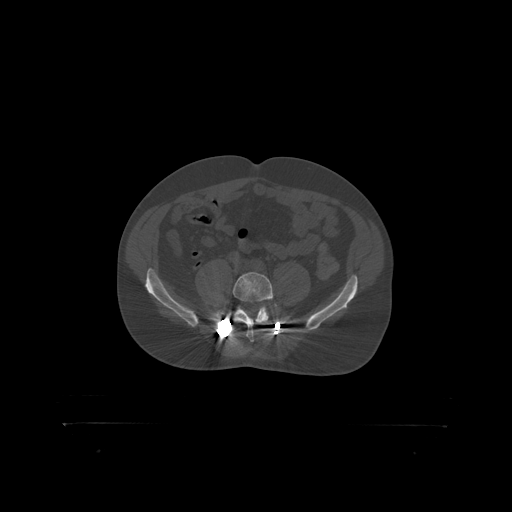
CT including the spine, one axial slice; position 203 of 399 along the scan axis; bone window (W 1800 / L 400 HU); 1.25 mm slice thickness; 512 × 512 image matrix, field of view 650 × 650 mm. Male patient, age 46 years. Case-level facts recorded for this patient, not image findings: primary cancer: skin.
Structures marked on this image (semi-automatic segmentation, software-assisted and operator-edited):
- L5 vertebra: bounding box [x1, y1, x2, y2] px = [233, 272, 278, 319]